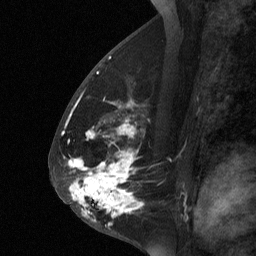
Breast MRI (dynamic contrast-enhanced), one sagittal slice. Dynamic contrast-enhanced study with each time point stored as its own series, time point 2 of 3 at this slice position (early post-contrast, ordered by acquisition time). 1.5 T. TE 4.8 ms, TR 27 ms. 2 mm slice thickness. 256 × 256 image matrix, field of view 180 × 180 mm. Female patient, age 56 years. From the clinical record (not read from this slice): setting: breast cancer imaged before/during neoadjuvant chemotherapy; receptor status: HER2-positive.
Outlined on this slice (semi-automatically segmented with operator editing):
- analysis volume of interest (the breast-tissue region the enhancement analysis was run in; not a lesion): bounding box <59,104,145,229> (left, top, right, bottom; pixels)
- tumour enhancement mask (voxels above the 90 % enhancement threshold inside the analysis volume of interest): <70,164,134,221>